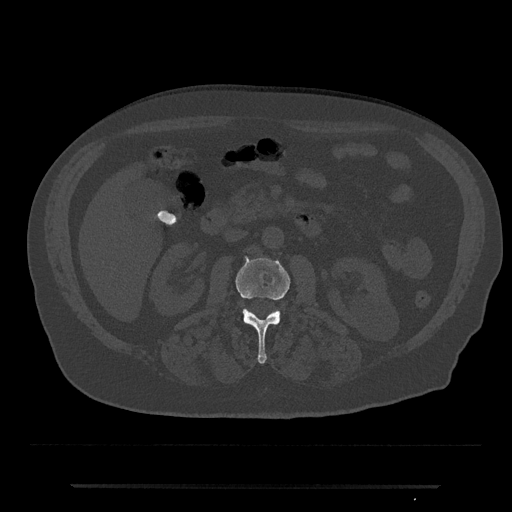
CT including the spine, one axial slice. Slice 463 of 797 in the series (ordered by position). Reconstruction kernel Br40s/3. Bone window (W 1800 / L 400 HU). 0.5 mm slice thickness. 512 × 512 image matrix. Male patient, age 80 years. Case-level facts recorded for this patient, not image findings: primary cancer: prostate.
Annotated regions visible in this slice (semi-automatic segmentation, software-assisted and operator-edited):
- L2 vertebra: bounding box <235,256,291,364> (left, top, right, bottom; pixels)